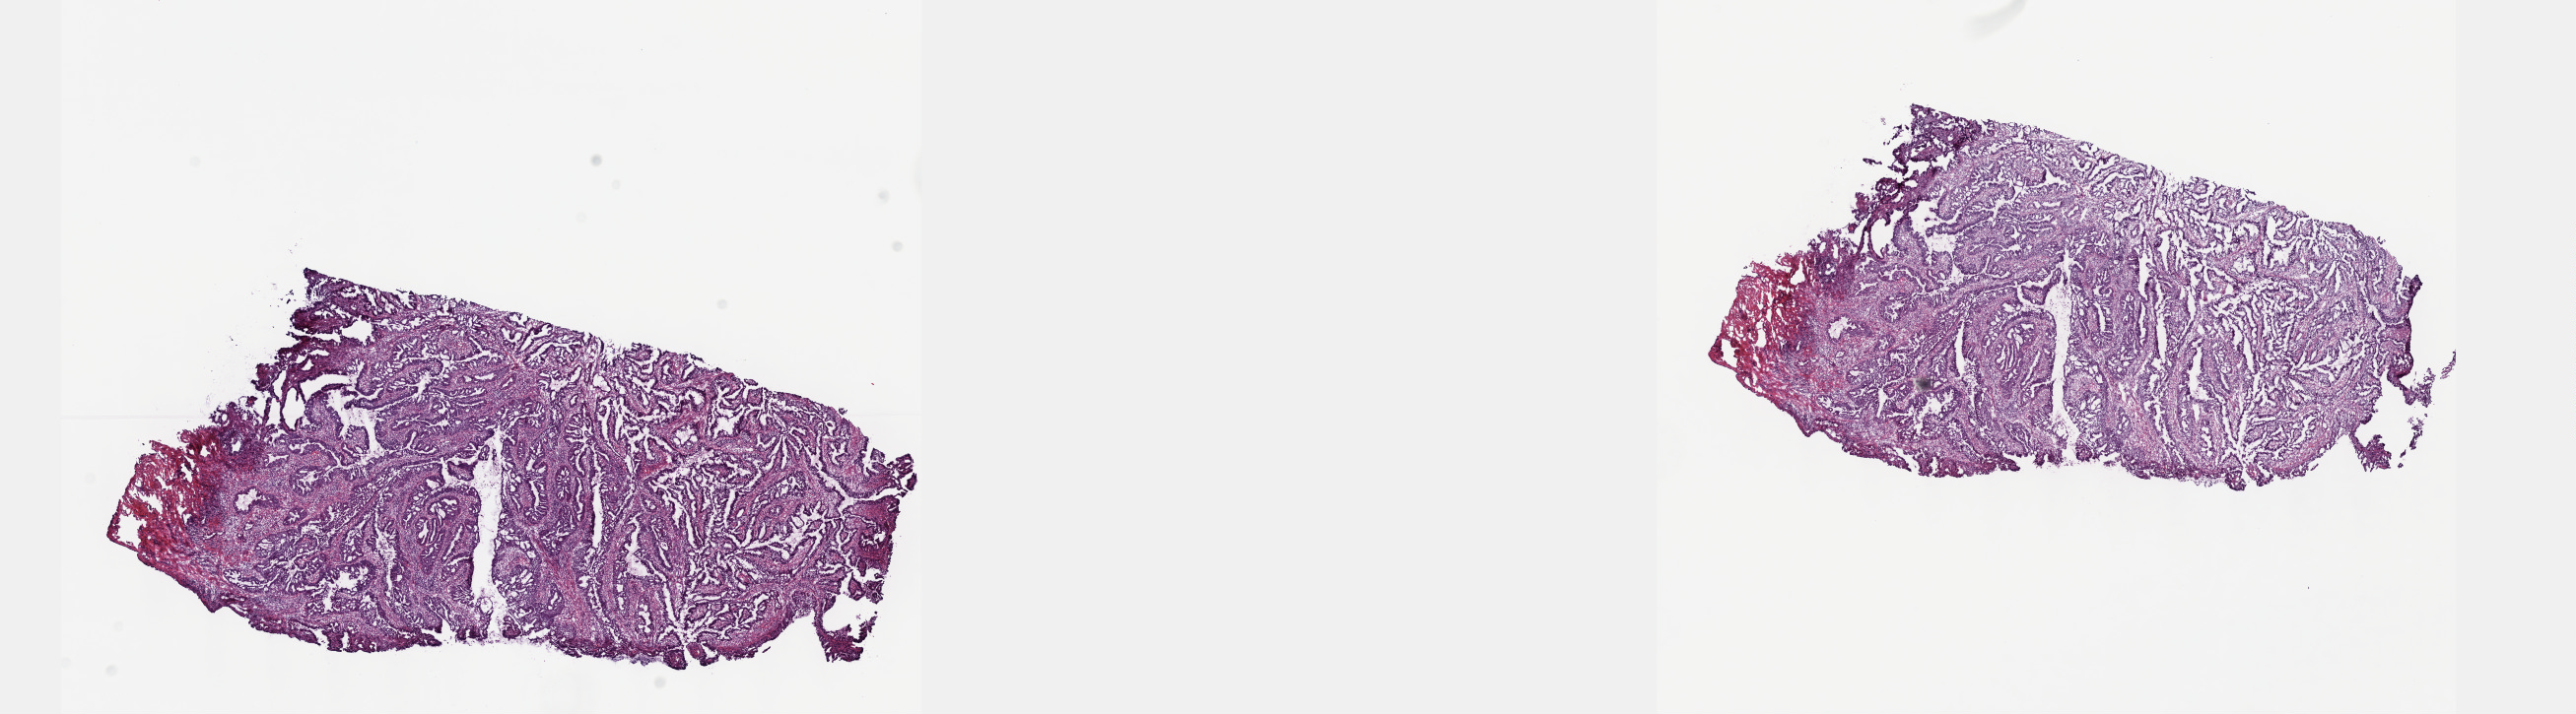
Digitized H&E tissue section (whole slide) — low-resolution overview of the scanned area, about 21.1 x 5.9 mm (from a 40x scan). Frozen section from the top of the tissue portion. Cervix, primary tumour sample. Patient: female, age at initial diagnosis 32 years. Histologic grade: G2 (moderately differentiated). Composition of this section per pathologist review: tumour cells 70%, tumour nuclei 70%, normal cells 0%, stromal cells 30%, necrosis 0%. Inflammatory infiltration, as recorded: lymphocyte infiltration 40%, monocyte infiltration 20%, neutrophil infiltration 20%.
FIGO stage: IB. Lymph nodes positive (case pathology): 0 of 22 examined. Histologic diagnosis: Mucinous adenocarcinoma, endocervical type.